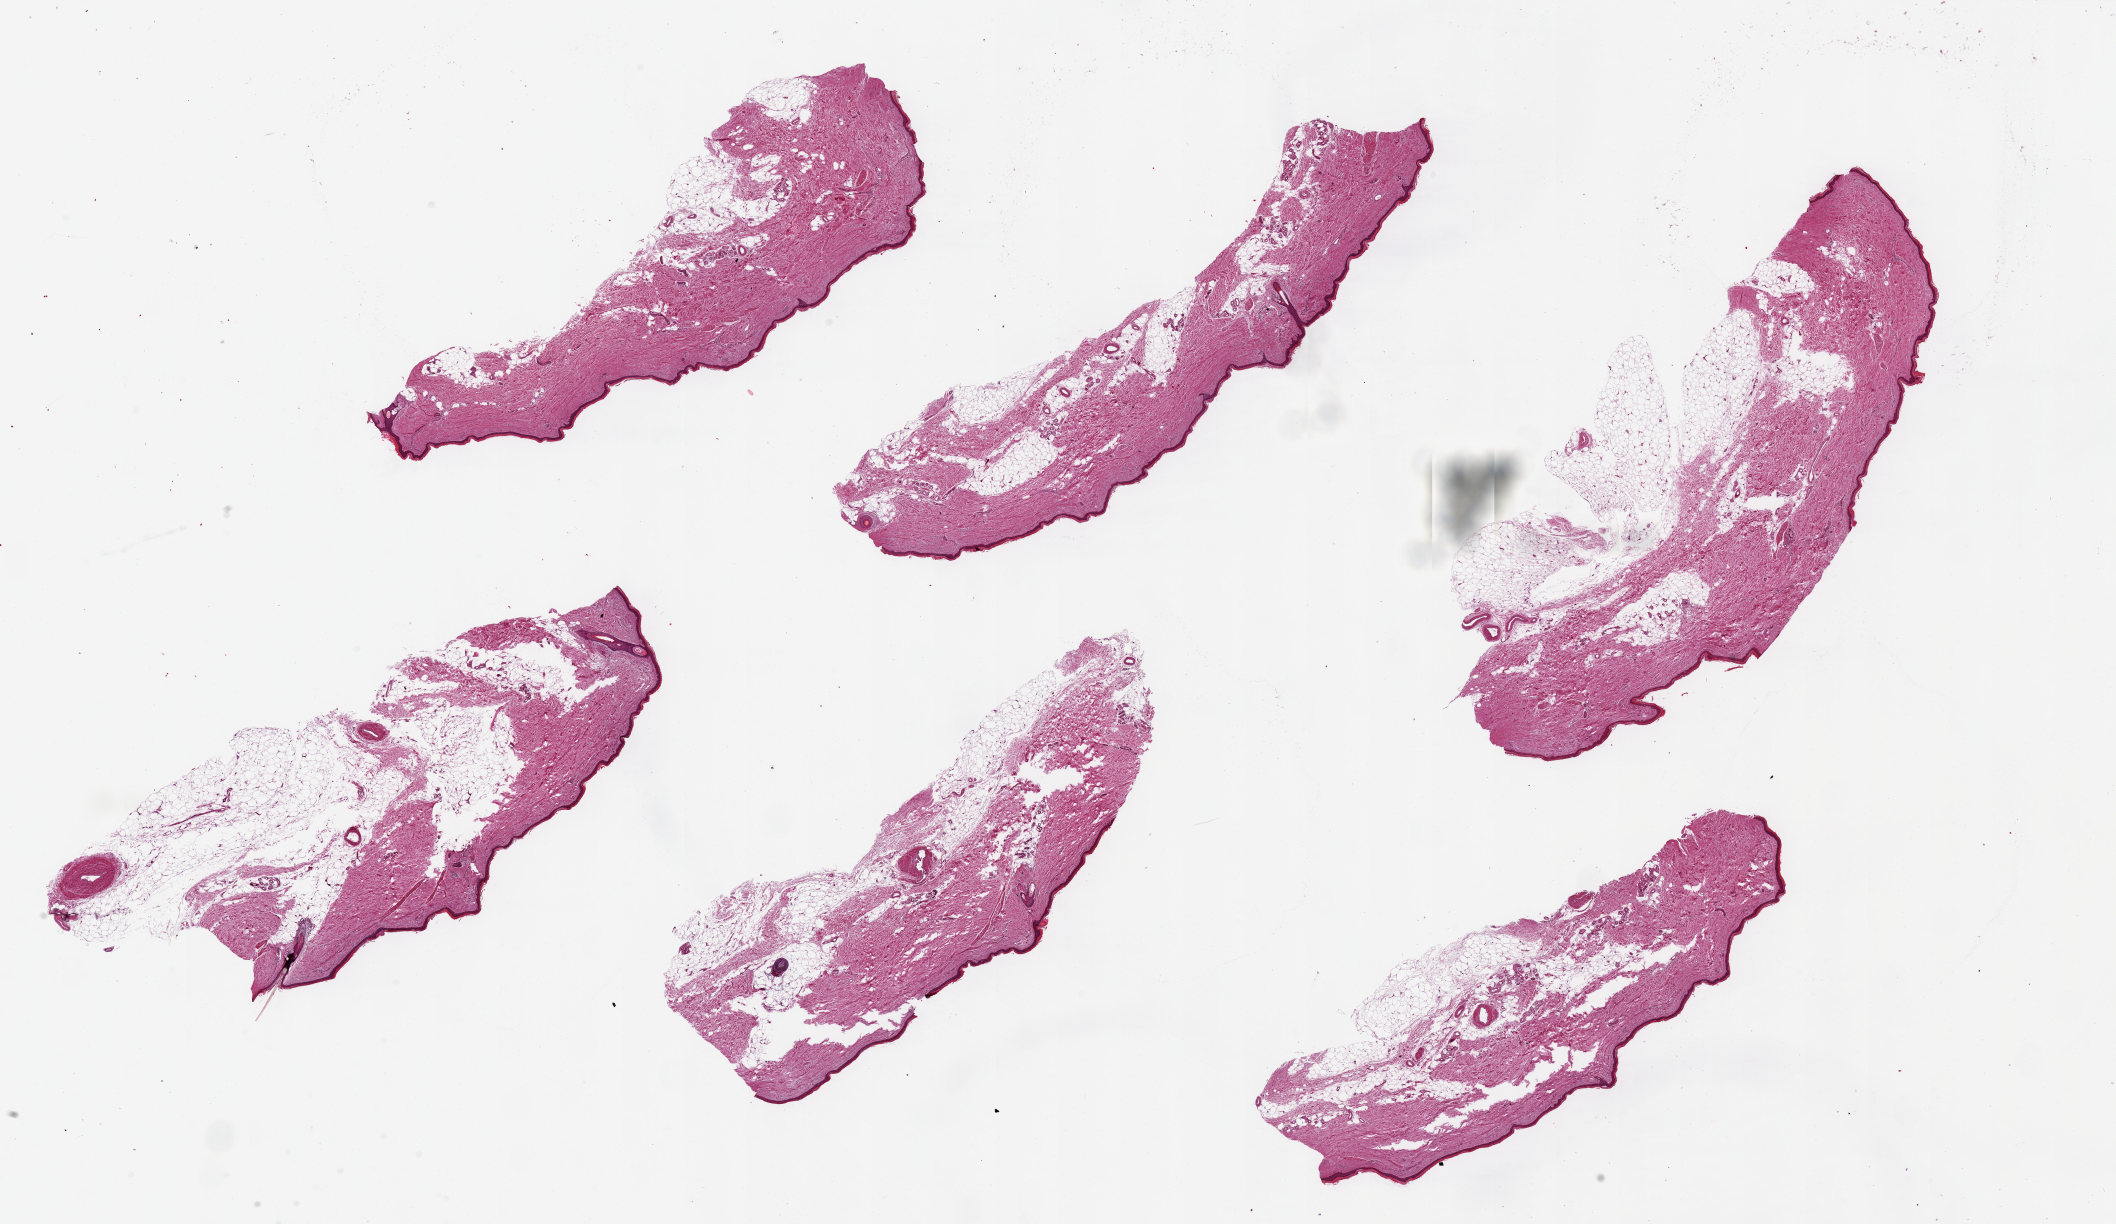
Digitized hematoxylin and eosin (H&E)-stained section, a low-resolution overview of the entire scanned area, about 33.5 x 19.4 mm, PAXgene-fixed, paraffin-embedded tissue, sampled site (target tissue): skin of lower leg, tissue donor sample. Donor sex: male.
Pathologist's review note for this sample: 6 pieces, up to 11x3mm; squamous epithelium is ~1% thickness.